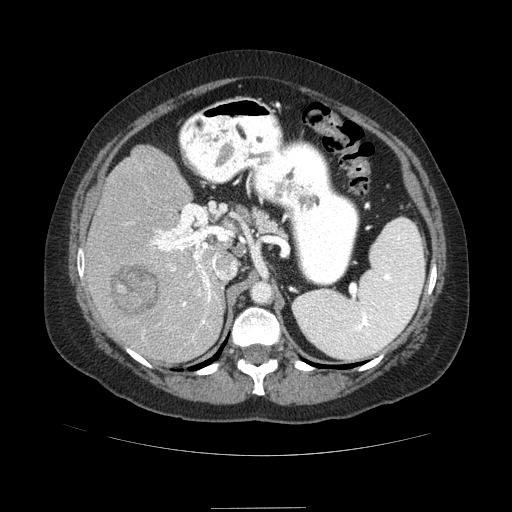
Contrast-enhanced abdominal CT (liver protocol), one axial slice. Slice 52 of 89 in the series (ordered by position). Reconstruction kernel STANDARD. 120 kVp. Soft-tissue window (W 400 / L 40 HU). 2.5 mm slice thickness. 512 × 512 image matrix, field of view 400 × 400 mm. From the clinical record (not read from this slice): diagnosis: hepatocellular carcinoma (patient treated with transarterial chemoembolisation; whether this scan precedes or follows treatment is not stated here); TNM stage (as recorded): Stage-IIIB; Child-Pugh class: A.
Annotated regions visible in this slice (semi-automatic segmentation, software-assisted and operator-edited):
- liver parenchyma outside the tumour (the mass and vessels are separate outlines, so this box may not span the whole liver): bounding box [x1, y1, x2, y2] px = [84, 146, 226, 363]
- mass: [108, 263, 160, 316]
- liver vessels: [150, 229, 218, 340]